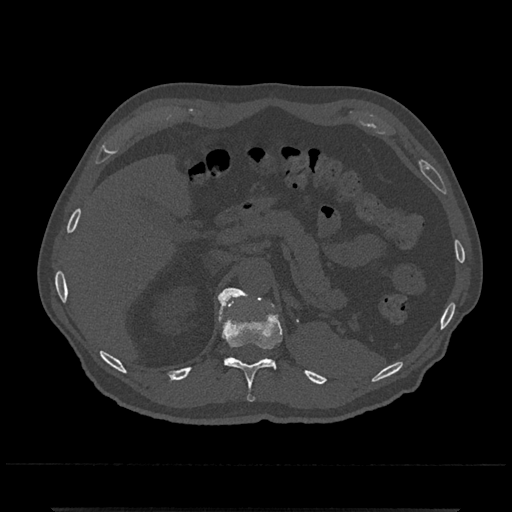
CT including the spine, one axial slice; slice 477 of 797 in the series (ordered by position); reconstruction kernel Br40s/3; 120 kVp; bone window (W 1800 / L 400 HU); 512 × 512 image matrix, field of view 393 × 393 mm. Patient: male, 67 years. Case-level facts recorded for this patient, not image findings: primary cancer: prostate.
Structures marked on this image (semi-automatic segmentation, software-assisted and operator-edited):
- T11 vertebra: box from (x=219, y=296) to (x=282, y=402) px
- T12 vertebra: (x=219, y=288)–(x=249, y=307)